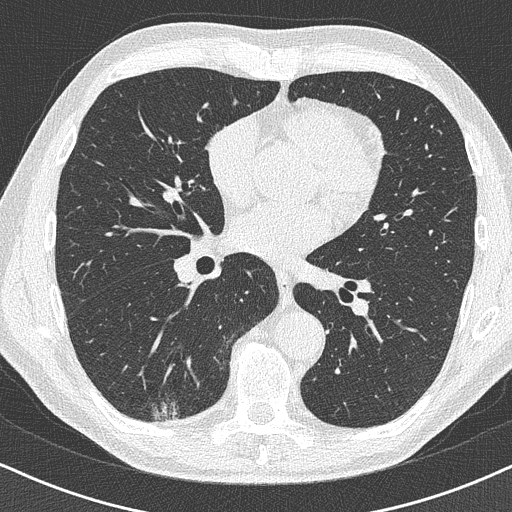
Axial slice from a low-dose chest CT screening exam. Baseline screening round. Lung window (W 1500 / L -600 HU). 1 mm slice thickness. 120 kVp. 512 × 512 image matrix. Male, age 63 years at enrolment.
Expert reader's lesion annotation, box from (x=127, y=357) to (x=199, y=427) px. Reader record for this screening exam (exam-level; its link to the box is not recorded): non-calcified nodule or mass ≥4 mm, right lower lobe, 16 × 13 mm, poorly defined margins. Later outcome: lung cancer diagnosed 74 days after this screen — adenocarcinoma, NOS, right lower lobe, moderately differentiated (G2), stage IA (AJCC 6th edition), 20 mm at pathology.